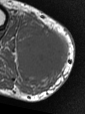
MRI of an extremity soft-tissue mass, one axial slice. Slice 29 of 47 in the series (ordered by position). MR volume resampled by the dataset authors to the PET/CT grid (not the native acquisition matrix). 3.27 mm slice thickness. 85 × 114 image matrix. Male patient. Case-level facts recorded for this patient, not image findings: histological type: pleiomorphic liposarcoma; grade: high; site of the primary tumour: right calf.
Structures marked on this image (expert contour drawn on MRI and transferred to this co-registered scan by the dataset authors):
- gross tumour volume including surrounding oedema: bounding box (x1, y1, x2, y2) in pixels: (19, 23, 69, 83)
- gross tumour volume (mass): (22, 30, 69, 79)